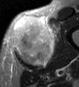
MRI of an extremity soft-tissue mass, one axial slice. Slice 19 of 45 in the series (ordered by position). STIR. MR volume resampled by the dataset authors to the PET/CT grid (not the native acquisition matrix). 3.27 mm slice thickness. 79 × 87 image matrix, field of view 77 × 85 mm. Male patient. Case-level facts recorded for this patient, not image findings: histological type: pleiomorphic leiomyosarcoma; grade: high; site of the primary tumour: left thigh.
Outlined on this slice (expert contour drawn on MRI and transferred to this co-registered scan by the dataset authors):
- gross tumour volume including surrounding oedema: box from (x=9, y=14) to (x=60, y=67) px
- gross tumour volume (mass): (x=9, y=16)–(x=55, y=67)